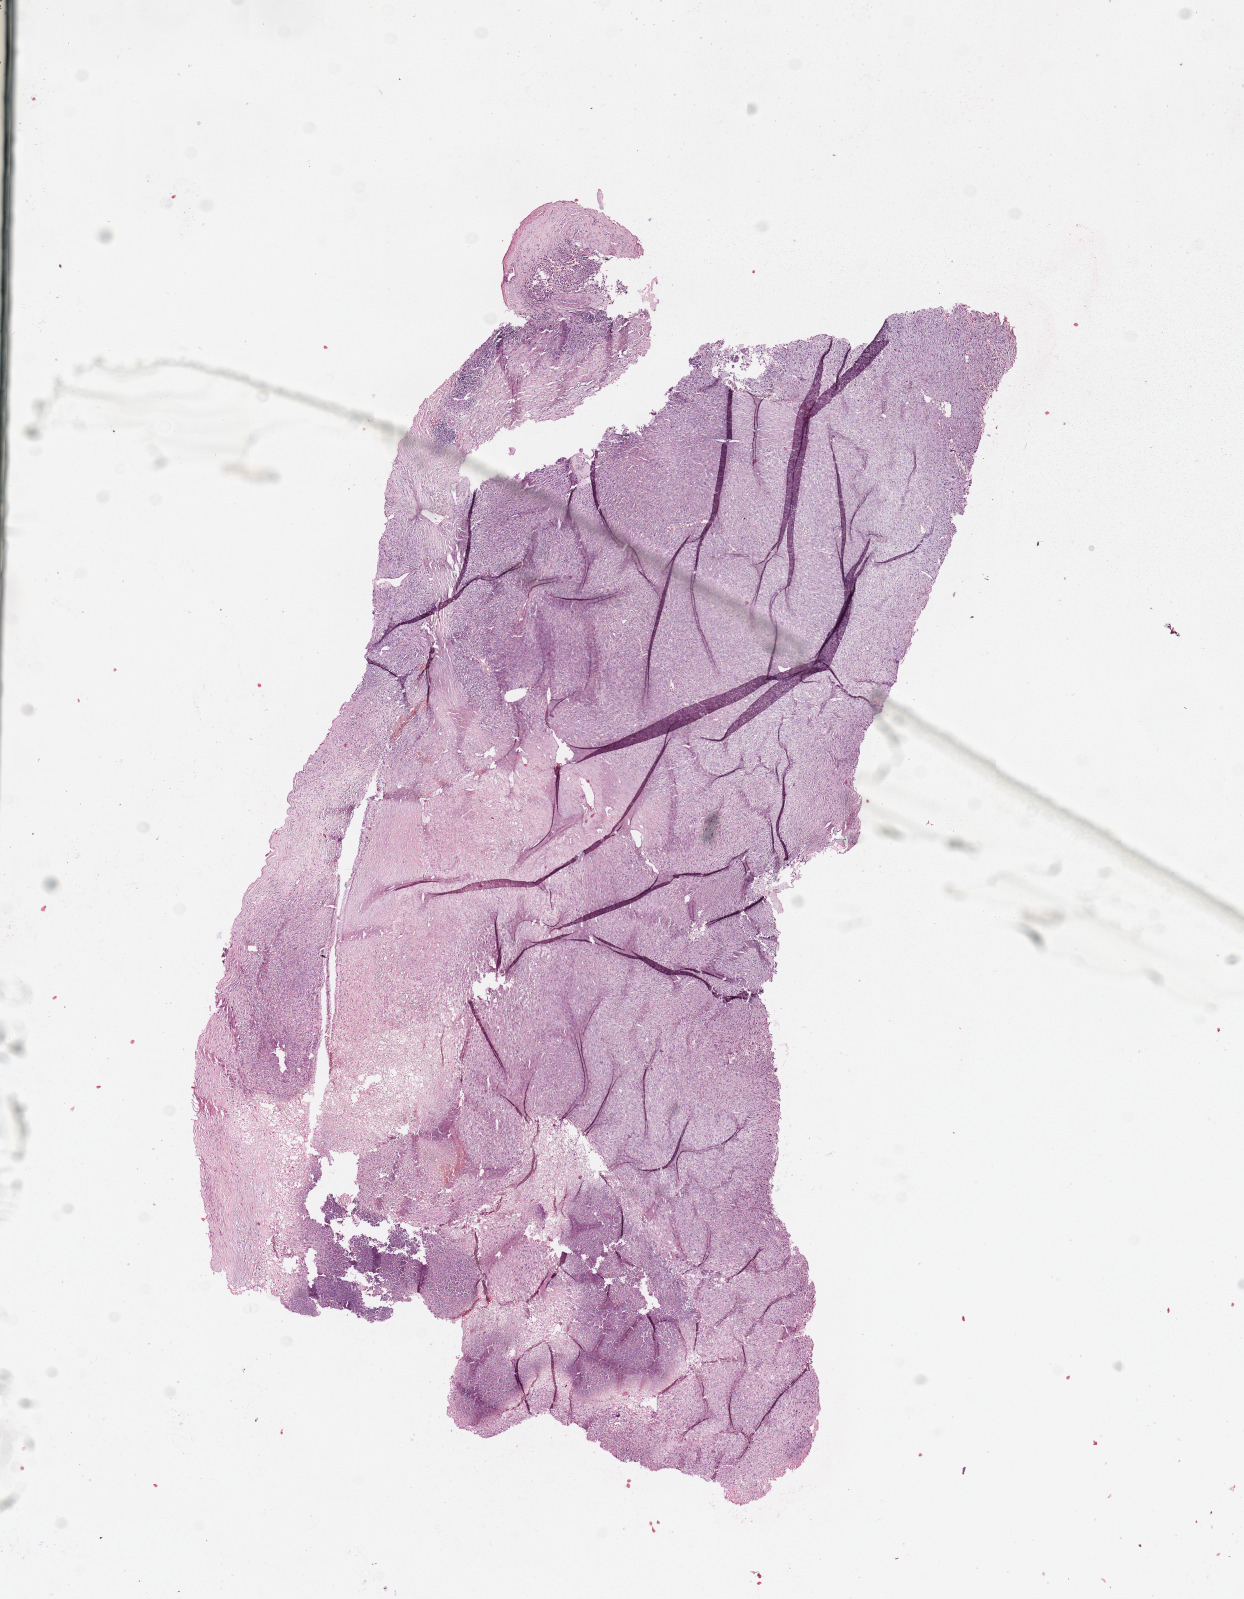
H&E-stained whole-slide image, whole scanned area (about 9.8 x 12.7 mm) shown as a low-resolution overview. Tumour tissue sample. Male, 53 y/o.
* patient diagnosis (cohort enrolment): sarcoma (site not recorded at cohort level)